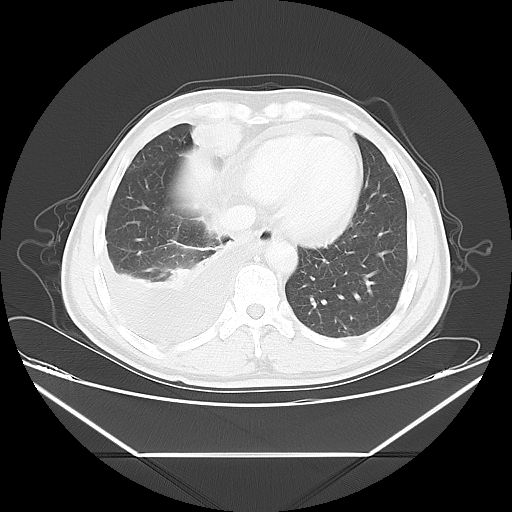
Chest CT, one axial slice; slice 14 of 56 in the series (ordered by position); reconstruction kernel LUNG; lung window (W 1500 / L -600 HU); 5 mm slice thickness; 512 × 512 image matrix. Patient: male, 57 years. Case-level facts recorded for this patient, not image findings: clinical TNM (as recorded): T2 N3 M1.
Annotated regions visible in this slice (rectangle marked by the reading radiologist):
- lung tumour (recorded histology: adenocarcinoma): bounding box <187,114,244,160> (left, top, right, bottom; pixels)